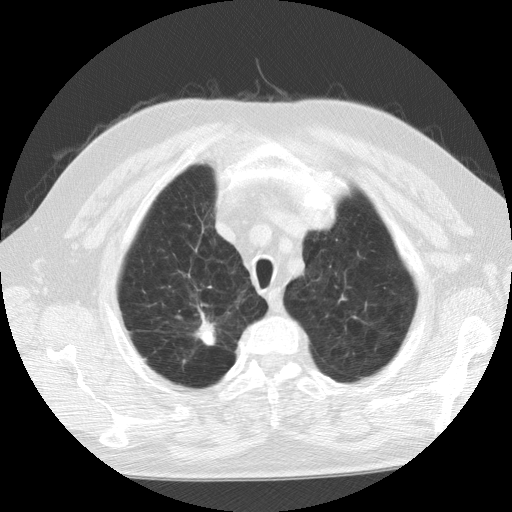
Low-dose screening chest CT, axial slice; second screening round (one year after baseline); lung window (W 1500 / L -600 HU); standard (soft-tissue) reconstruction kernel (STANDARD); slice 17 of 109 in the series. Male, age 64 years at enrolment. Current smoker at enrolment.
Expert reader's lesion annotation, bounding box (x1, y1, x2, y2) in pixels: (183, 315, 232, 359). The screening reader recorded 2 non-calcified nodules or masses ≥4 mm on this exam (left upper lobe, right lower lobe); which of them this box marks is not recorded. Lung cancer was diagnosed 233 days after this screen: squamous cell carcinoma, NOS, left upper lobe, moderately differentiated (G2), stage IA (AJCC 6th edition), 10 mm at pathology.